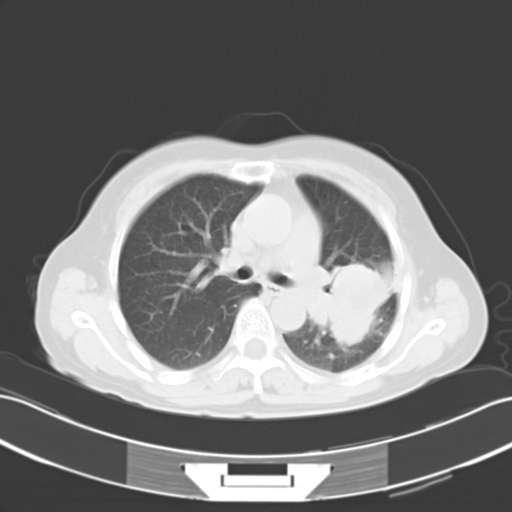
Chest CT, one axial slice; position 16 of 25 along the scan axis; reconstruction kernel B40f; 120 kVp; lung window (W 1500 / L -600 HU); 512 × 512 image matrix, field of view 353 × 353 mm. Patient: female, 54 years. Case-level facts recorded for this patient, not image findings: clinical TNM (as recorded): T3 N1 M0.
Structures marked on this image (rectangle marked by the reading radiologist):
- lung tumour (recorded histology: adenocarcinoma): bounding box (x1, y1, x2, y2) in pixels: (316, 250, 392, 350)